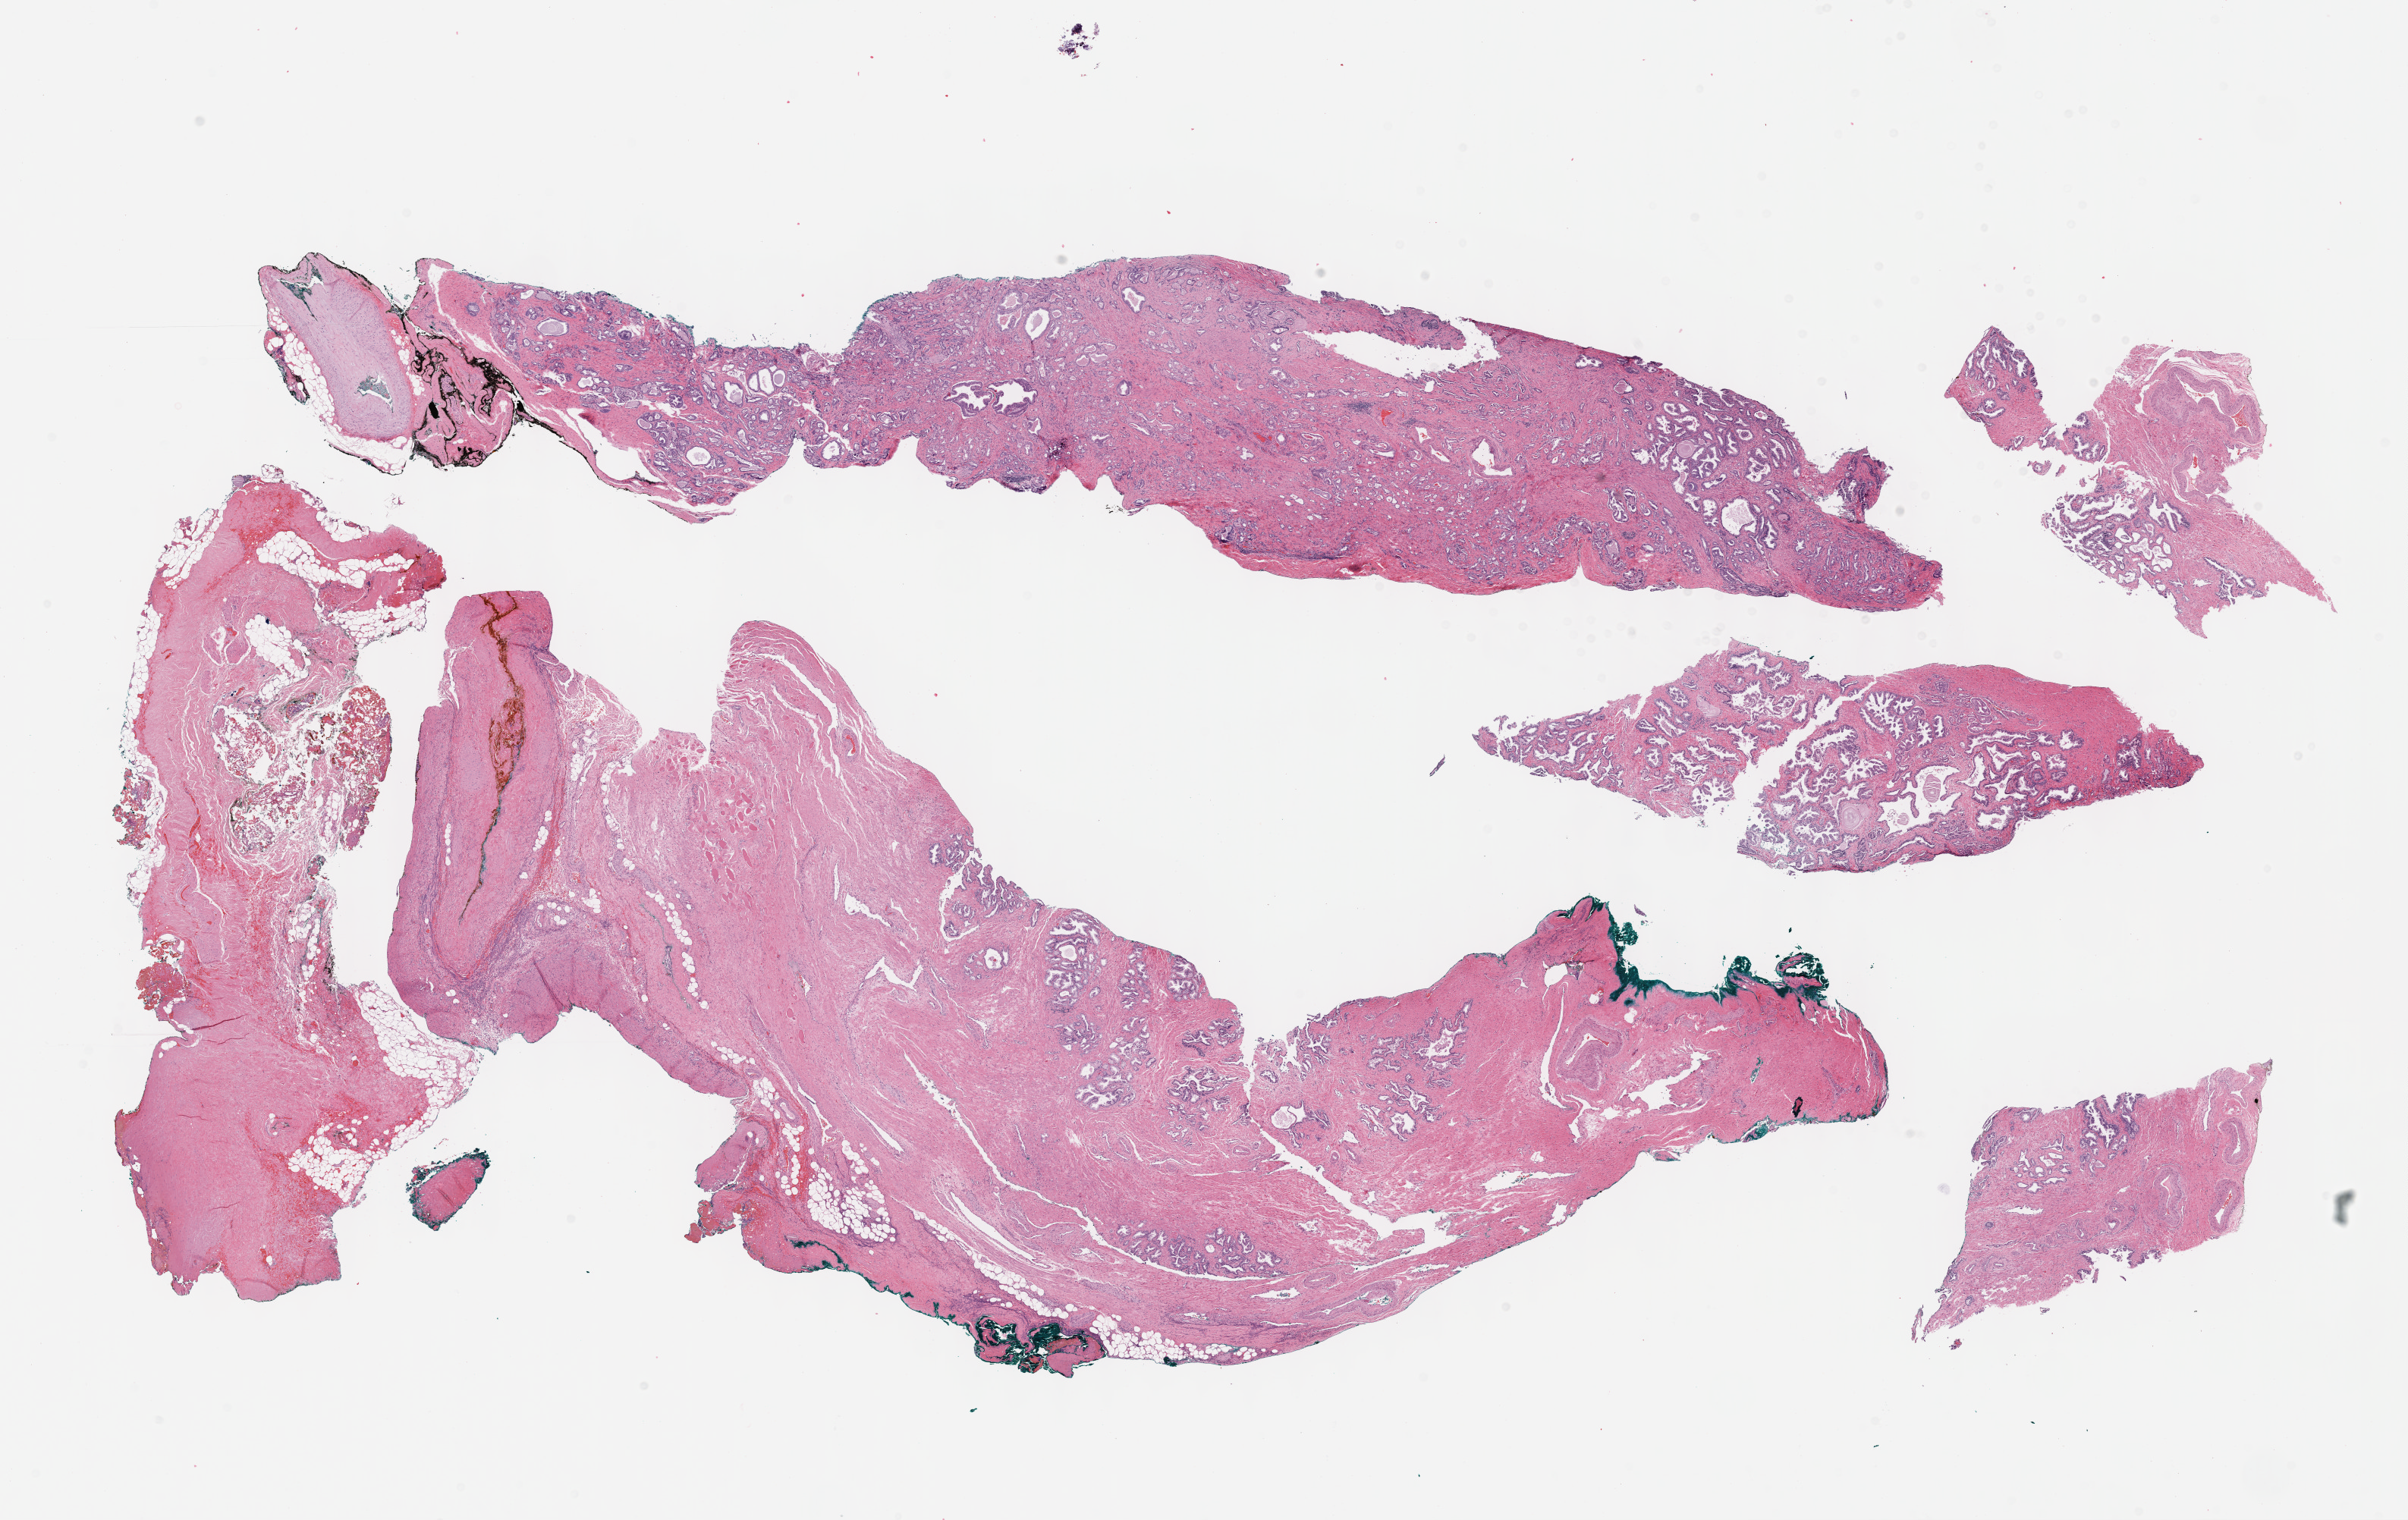
H&E-stained whole-slide image — shown as a low-resolution overview of the whole scanned area (about 25.7 x 16.2 mm). FFPE section. Primary tumour sample from the prostate. Male, age 58 years at initial diagnosis. Gleason score: 7 (3+4).
Pathologic diagnosis: Acinar cell carcinoma (prostate gland). Lymph nodes positive (case pathology): 0 of 6 examined.